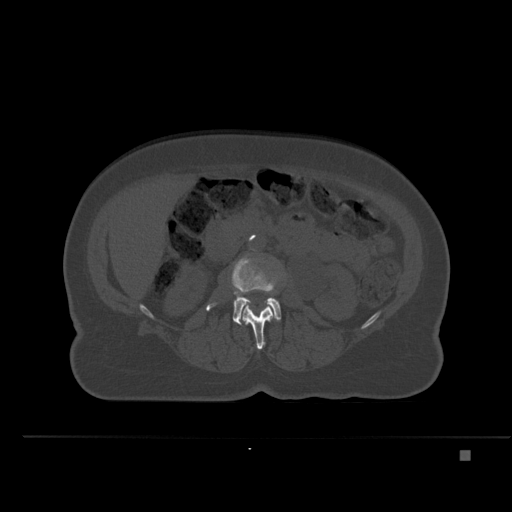
CT including the spine, one axial slice. Slice 207 of 477 in the series (ordered by position). Bone window (W 1800 / L 400 HU). 1.5 mm slice thickness. 512 × 512 image matrix. Patient: female, 74 years. From the clinical record (not read from this slice): primary cancer: colon.
Annotated regions visible in this slice (semi-automatic segmentation, software-assisted and operator-edited):
- L2 vertebra: bounding box (x1, y1, x2, y2) in pixels: (243, 305, 273, 350)
- L3 vertebra: (206, 258, 281, 324)